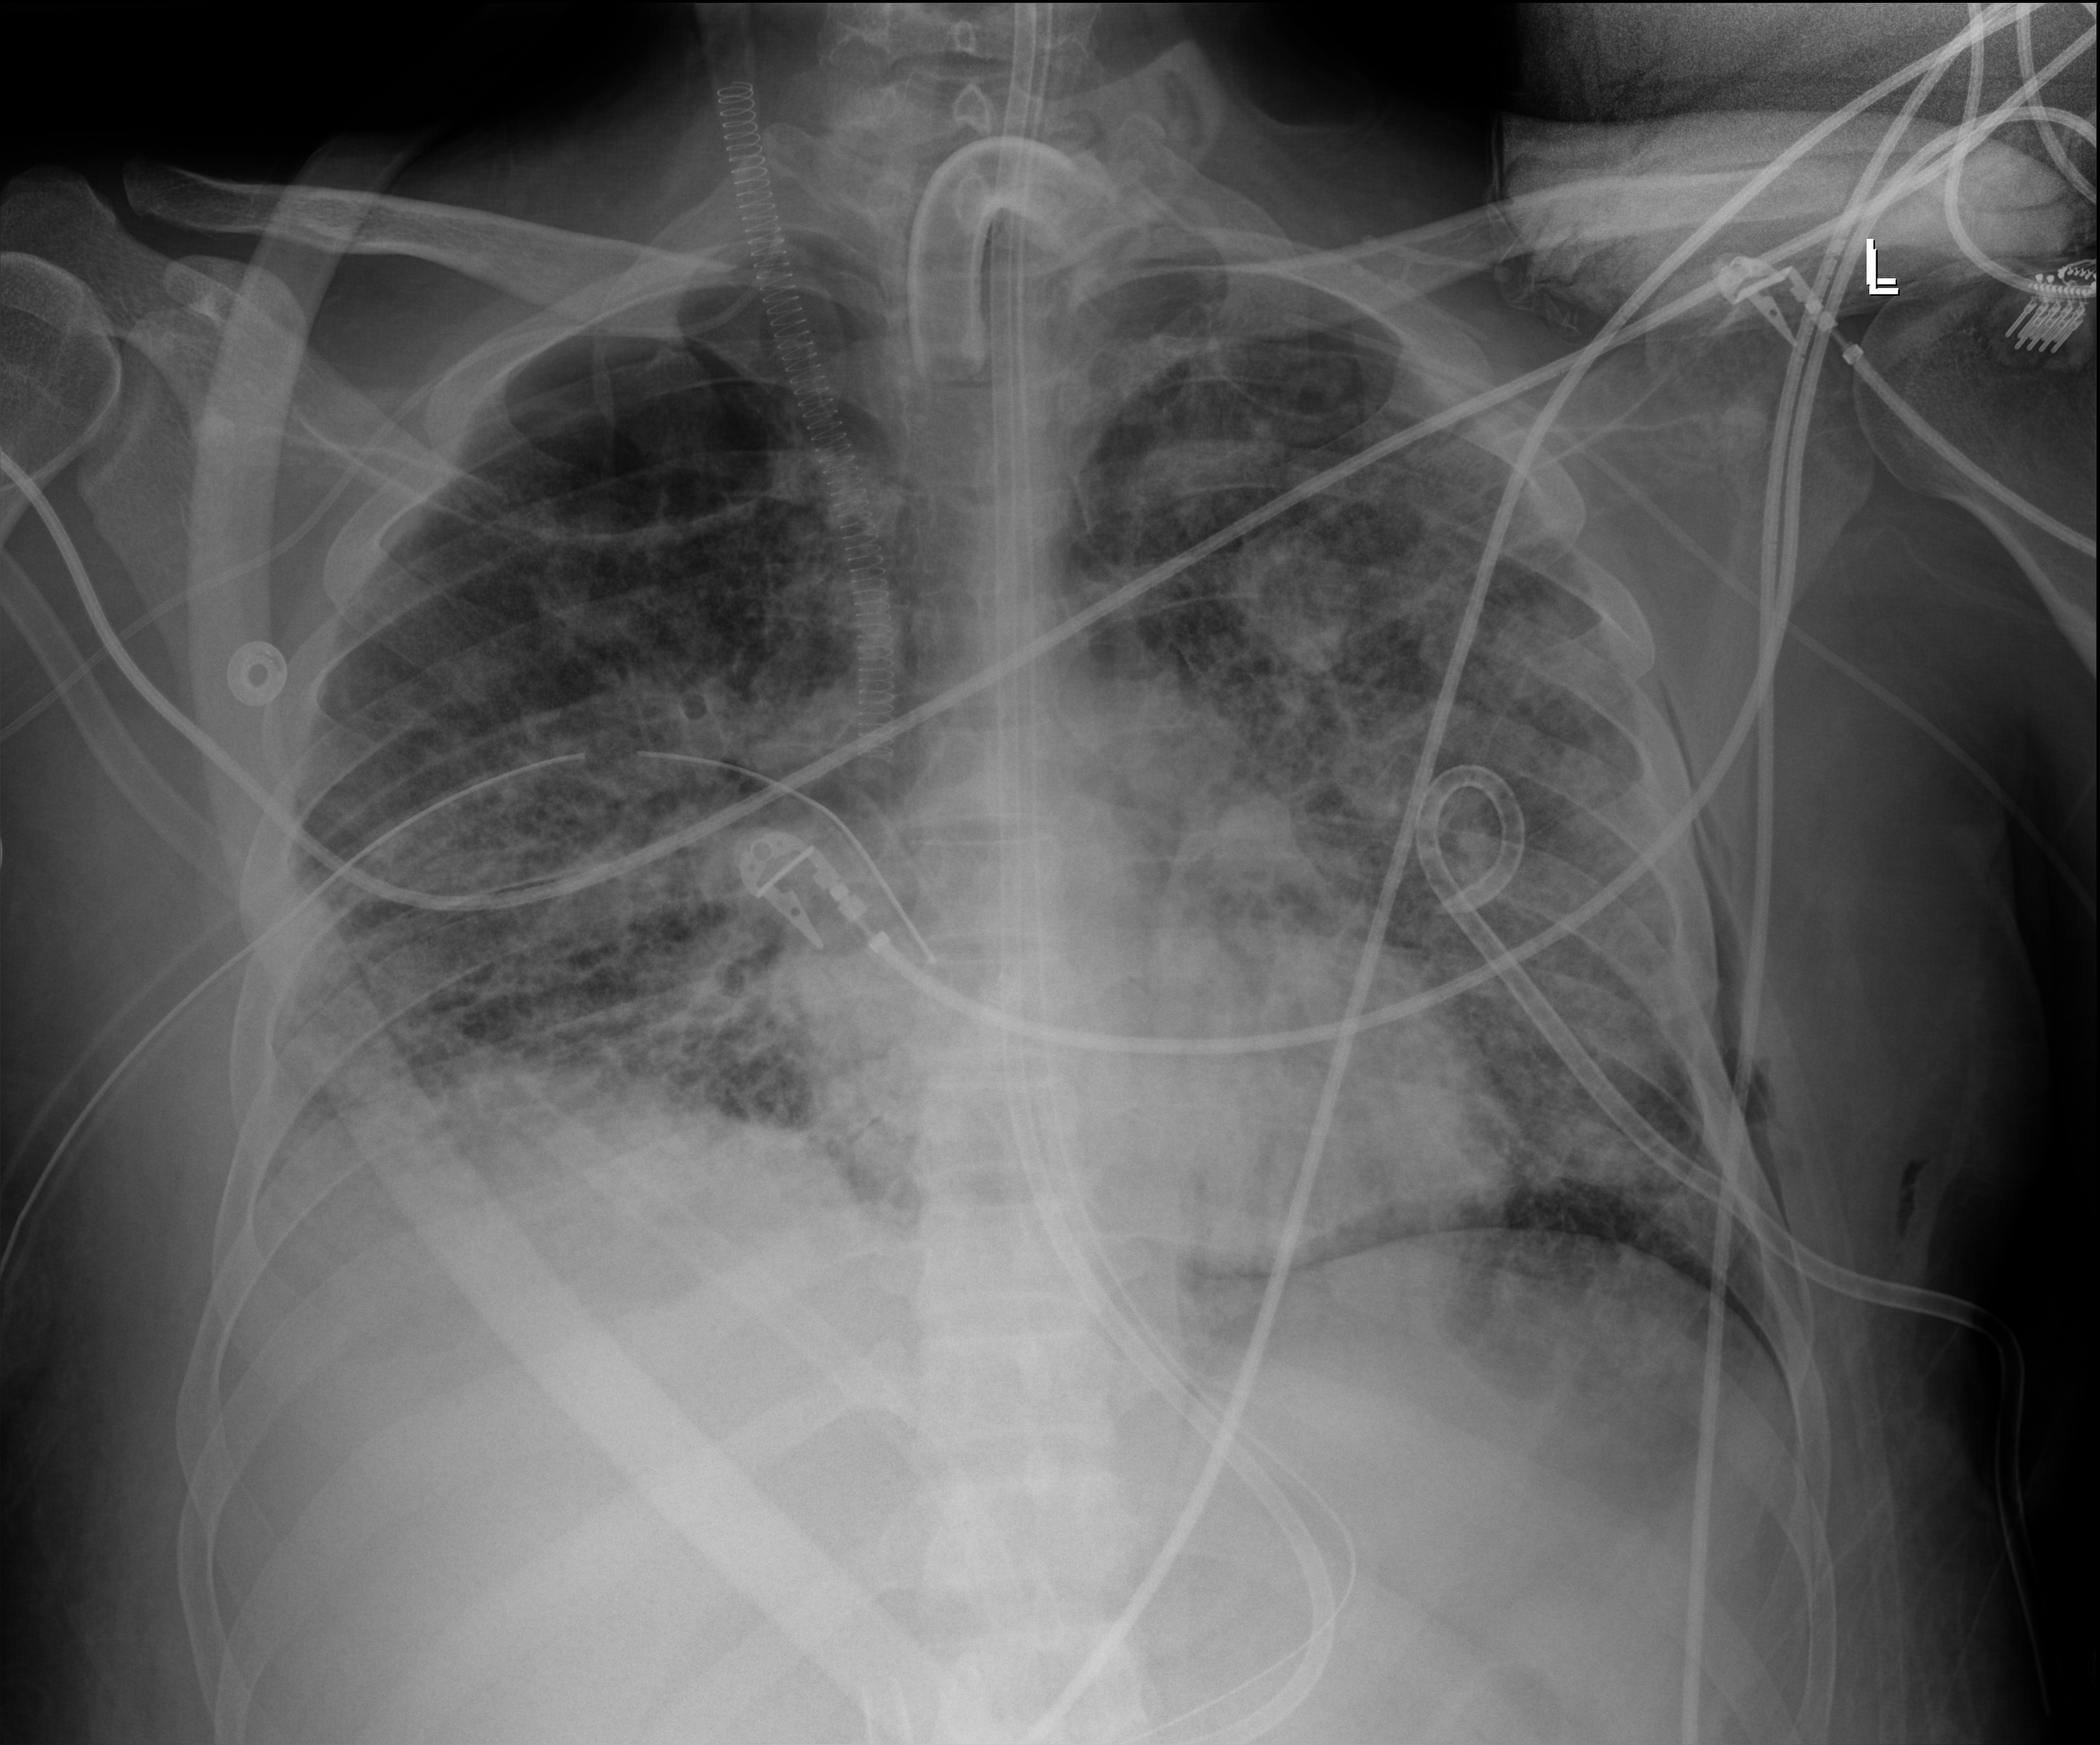
Chest X-ray; anteroposterior (AP) projection. Adult patient hospitalised with COVID-19, age 18–59 years.
Admission-level facts for this patient (not findings on this image; timing relative to this image not recorded): chronic kidney disease (admission record): no.